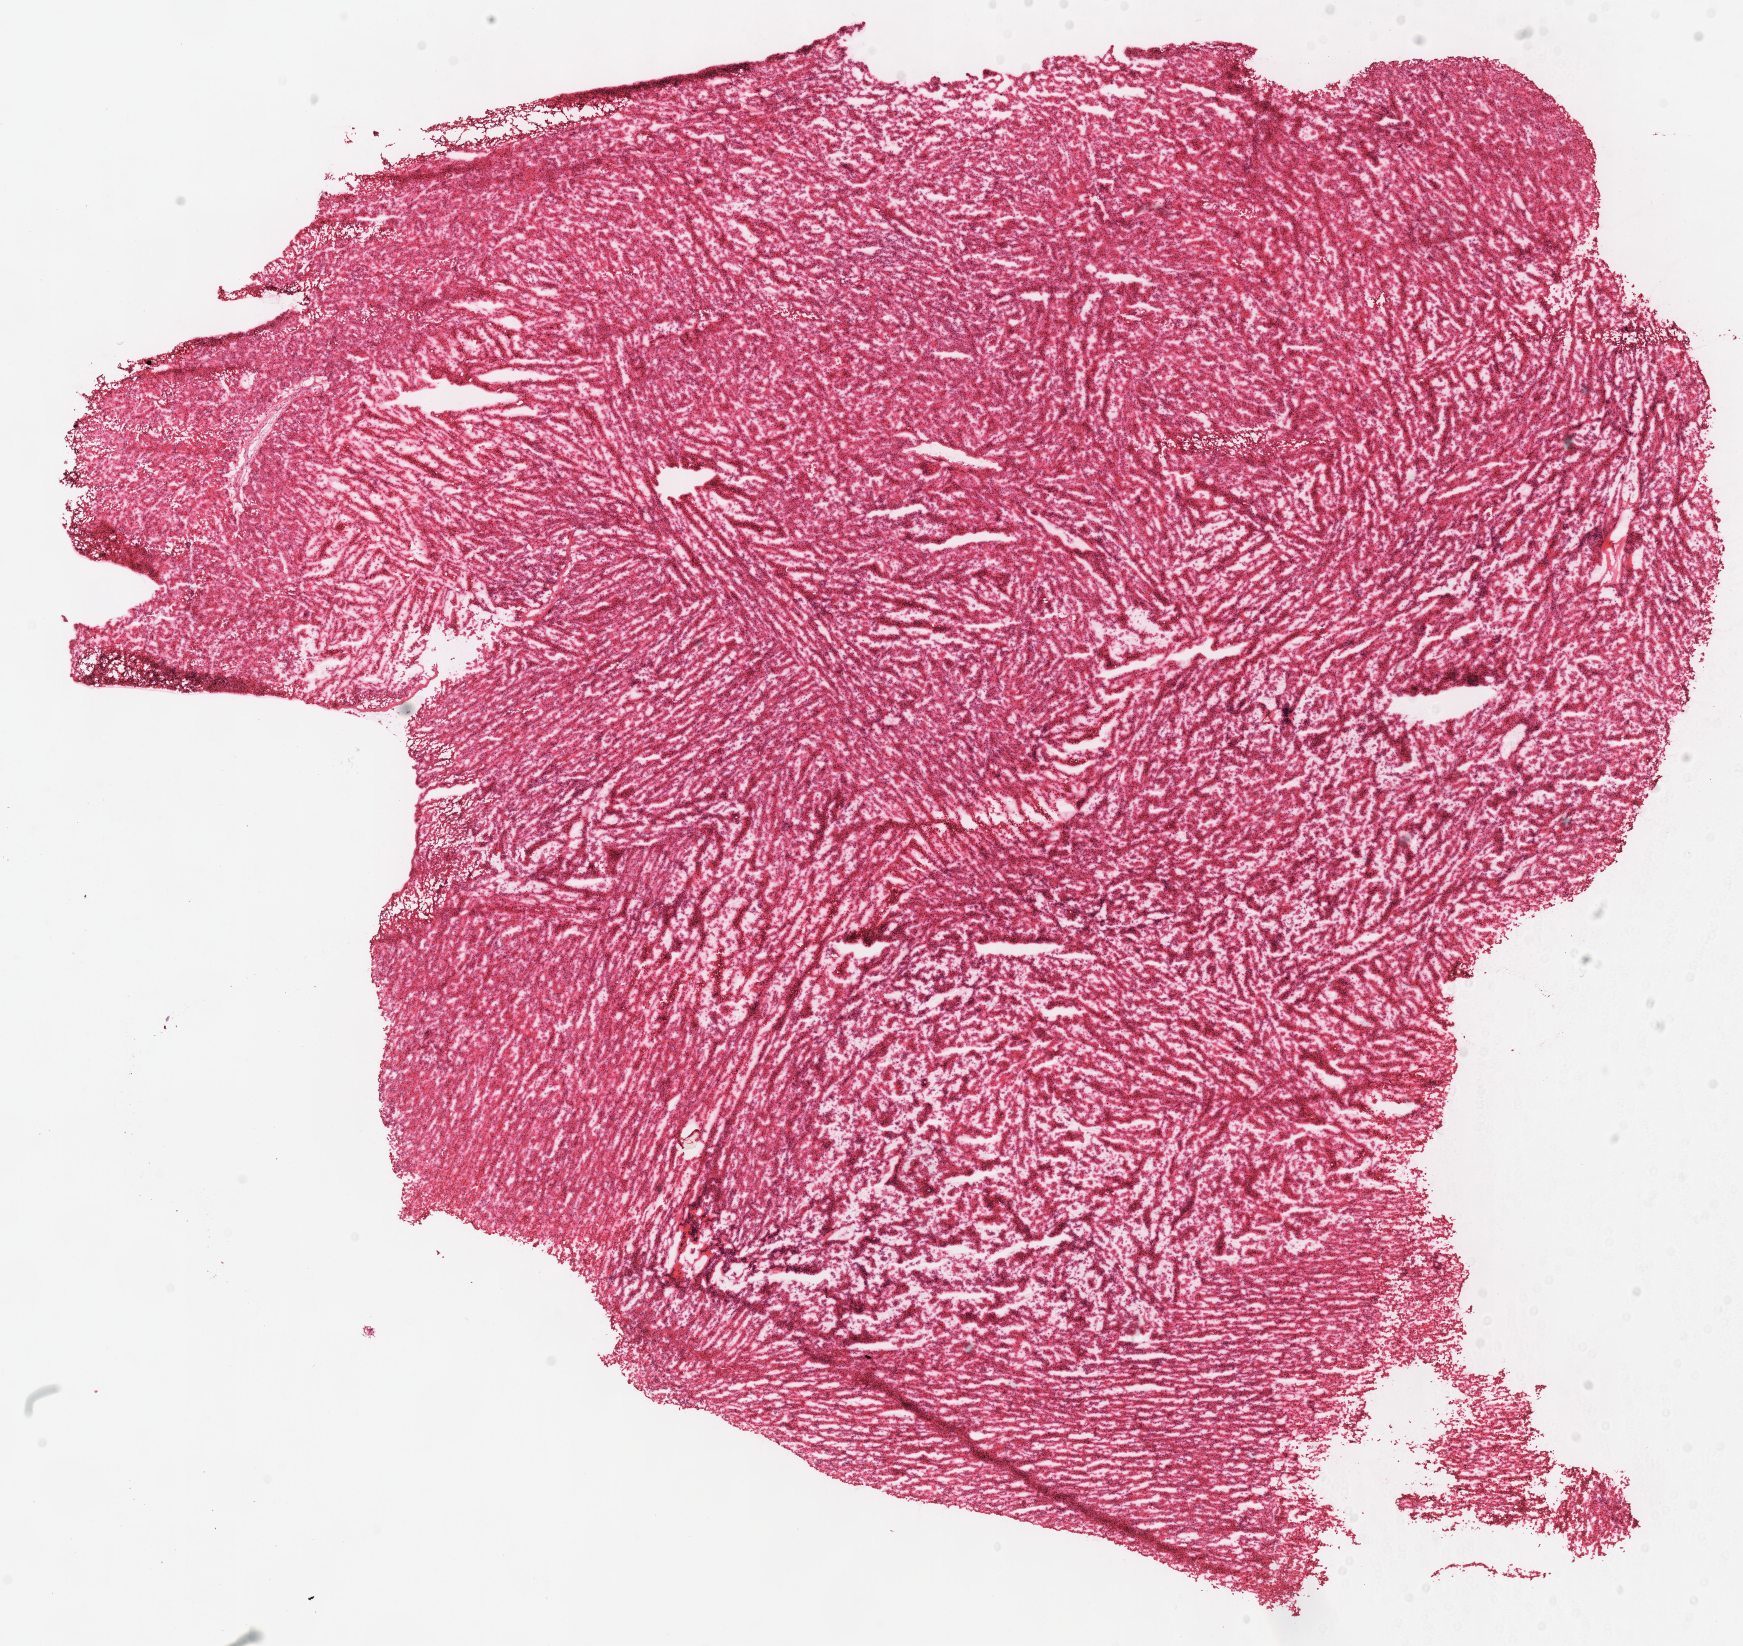
Digitized H&E-stained tissue section (whole slide) — whole scanned area (about 13.7 x 12.9 mm, from a 40x scan) shown as a low-resolution overview. Frozen section from the top of the tissue portion. Primary tumour sample from the kidney. Male patient; age at initial diagnosis 62 years. Composition of this section per pathologist review: tumour cells 100%, tumour nuclei 95%, normal cells 0%, stromal cells 0%, necrosis 0%. Infiltration values recorded for this section: lymphocyte infiltration 0%, monocyte infiltration 0%, neutrophil infiltration 0%.
• diagnosis: Renal cell carcinoma, chromophobe type
• laterality: right
• AJCC pathologic stage: II (6th edition)